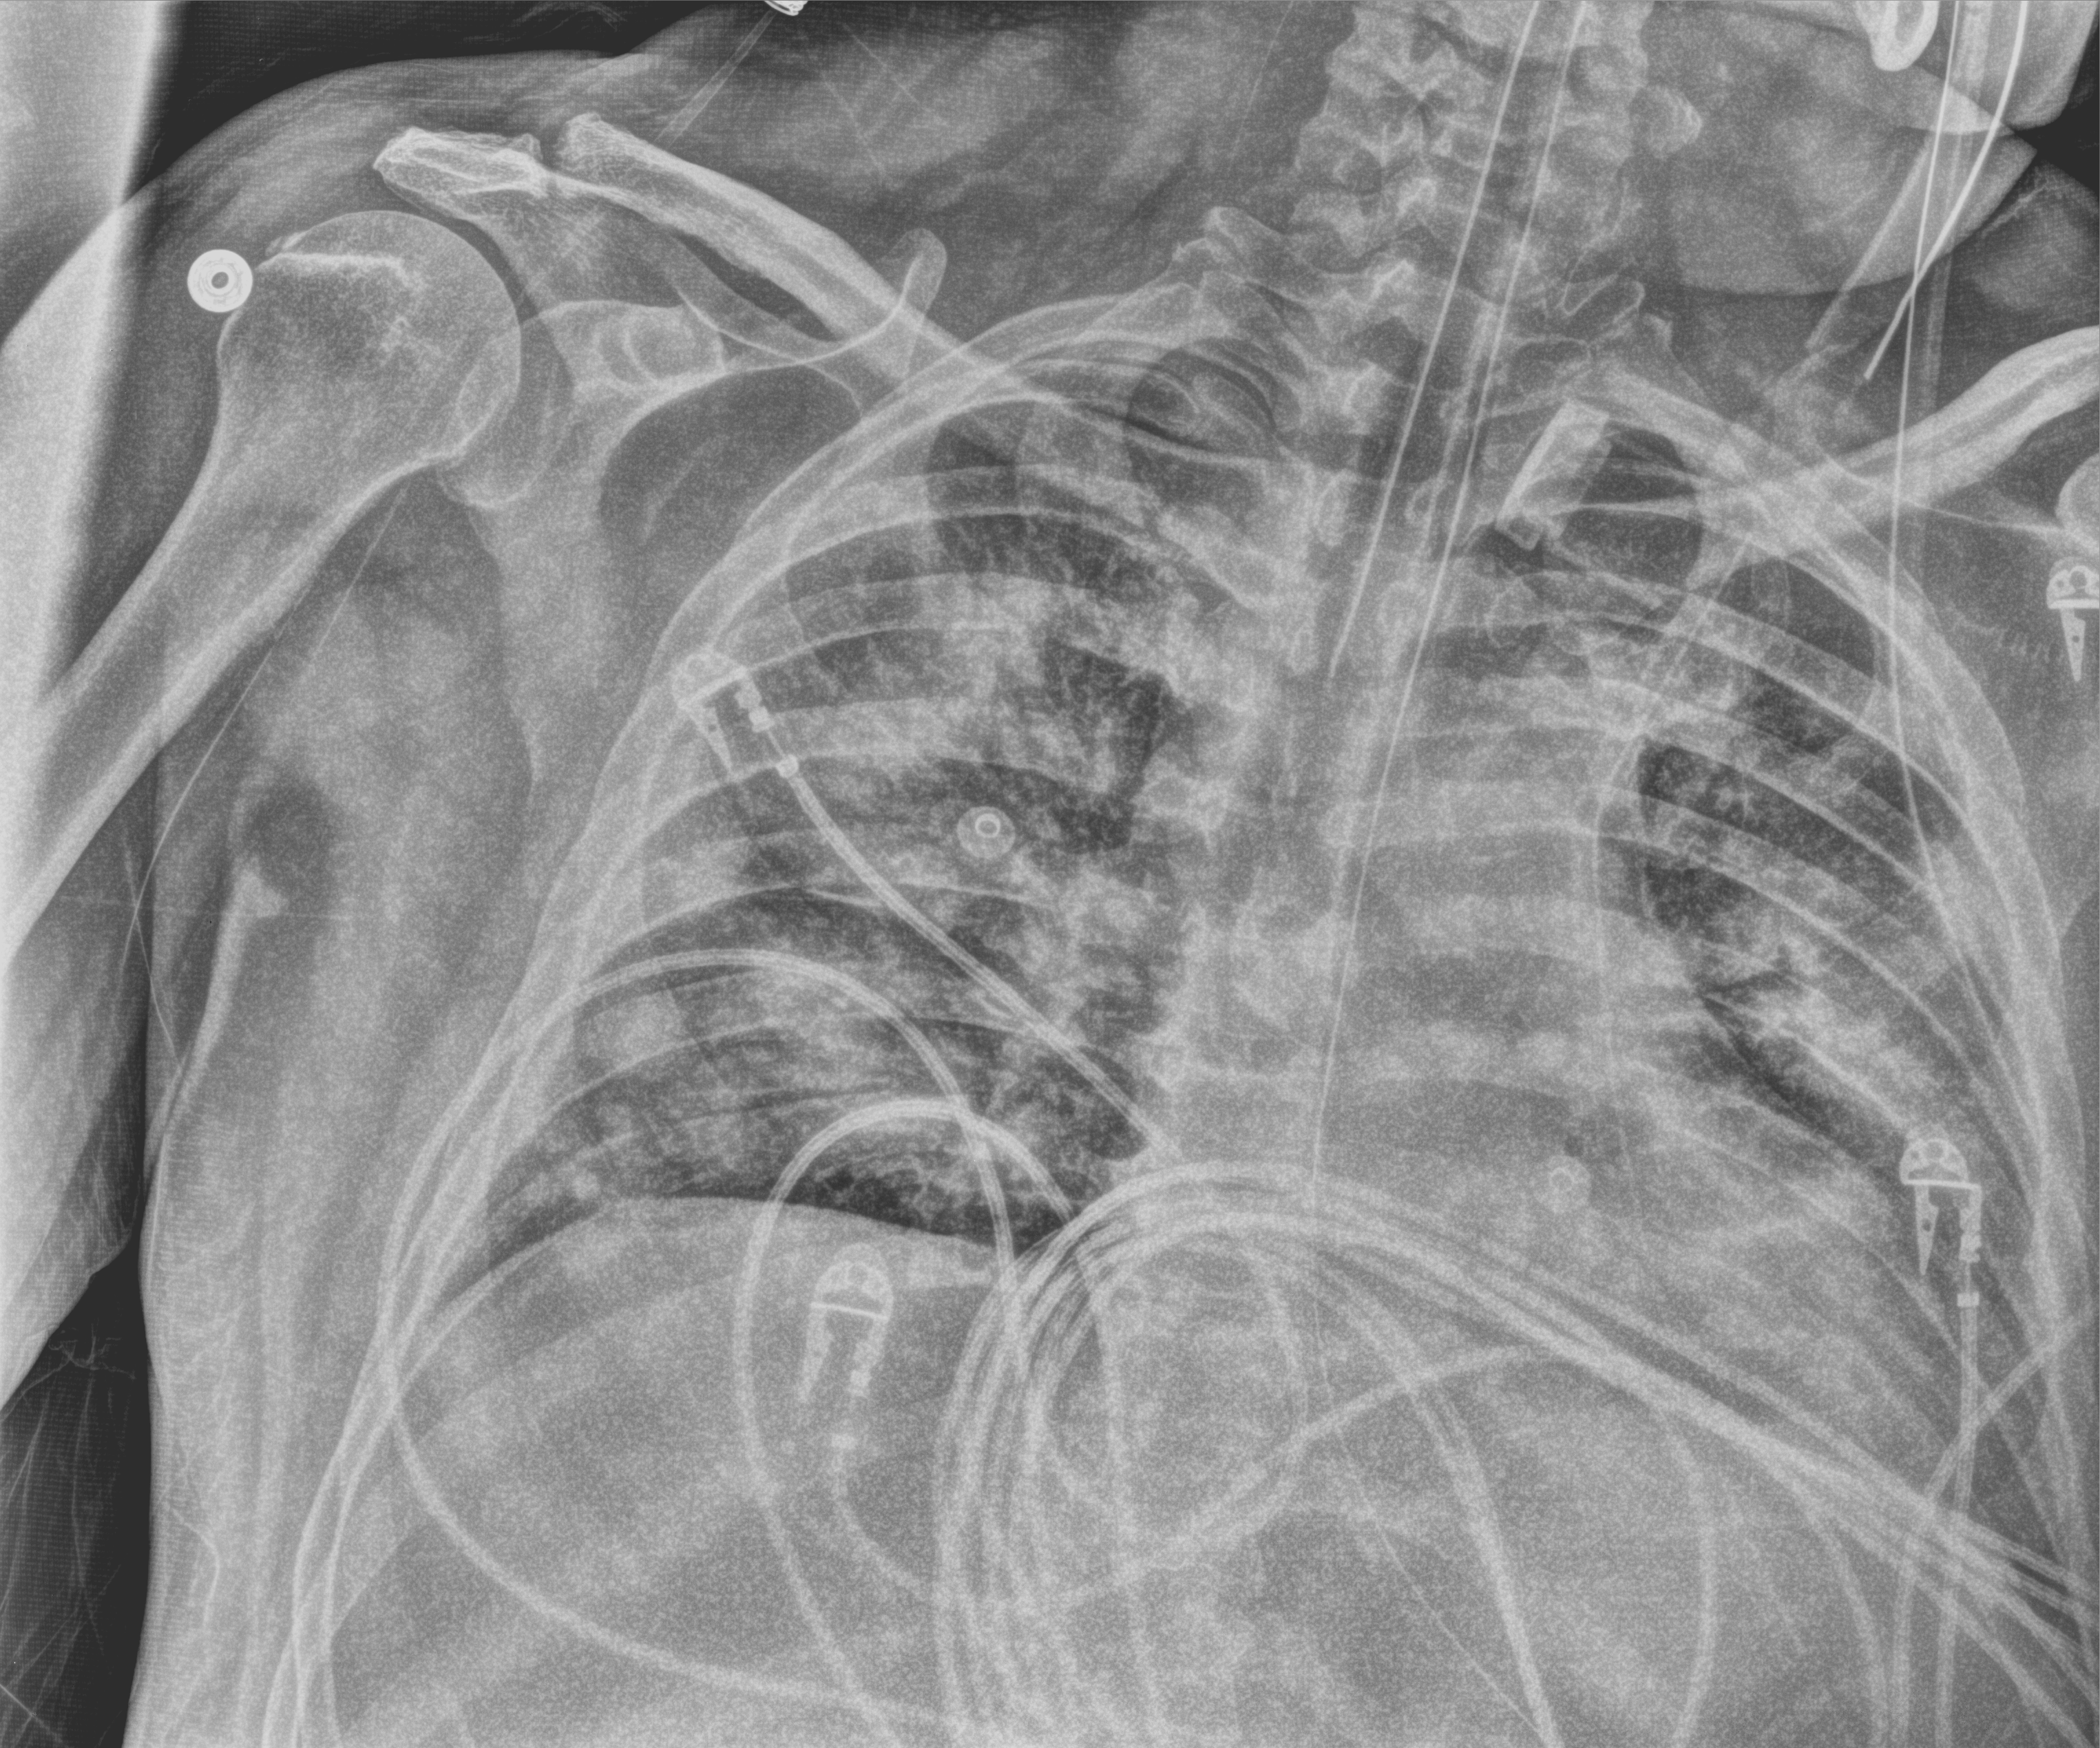
Portable chest radiograph; anteroposterior (AP) projection. Patient hospitalised with COVID-19; male, aged 18–59 years.
From the hospital-stay record, not from the radiograph (when in the stay this image was taken is not recorded): admitted to intensive care during this hospital stay: yes; mechanically ventilated during this hospital stay: yes.